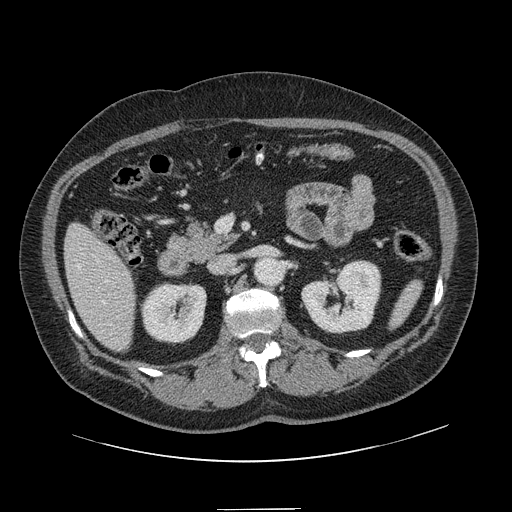
Contrast-enhanced abdominal CT, one axial slice; position 57 of 154 along the scan axis; 120 kVp; soft-tissue window (W 400 / L 40 HU); 512 × 512 image matrix, field of view 451 × 451 mm. Male patient, age 61 years. Case-level facts recorded for this patient, not image findings: diagnosis: colorectal cancer liver metastases, imaged before liver resection; multiple liver metastases: yes; largest metastasis: 2.6 cm; chemotherapy before resection: no.
Outlined on this slice (outlined manually by an expert reader):
- hepatic veins: bounding box (x1, y1, x2, y2) in pixels: (77, 265, 106, 305)
- liver: (65, 225, 136, 351)
- planned liver remnant (the part of the liver to remain after resection): (65, 225, 136, 352)